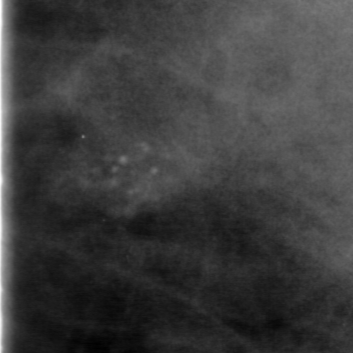
Crop from a digitized film mammogram around one marked abnormality; left breast; CC view; BI-RADS breast density category 3 (scale 1–4).
Finding: calcifications, morphology round and regular / pleomorphic, distribution clustered; BI-RADS assessment category 0; subtlety rating 3 on a 1 (subtle) to 5 (obvious) scale; pathology (as recorded): benign.